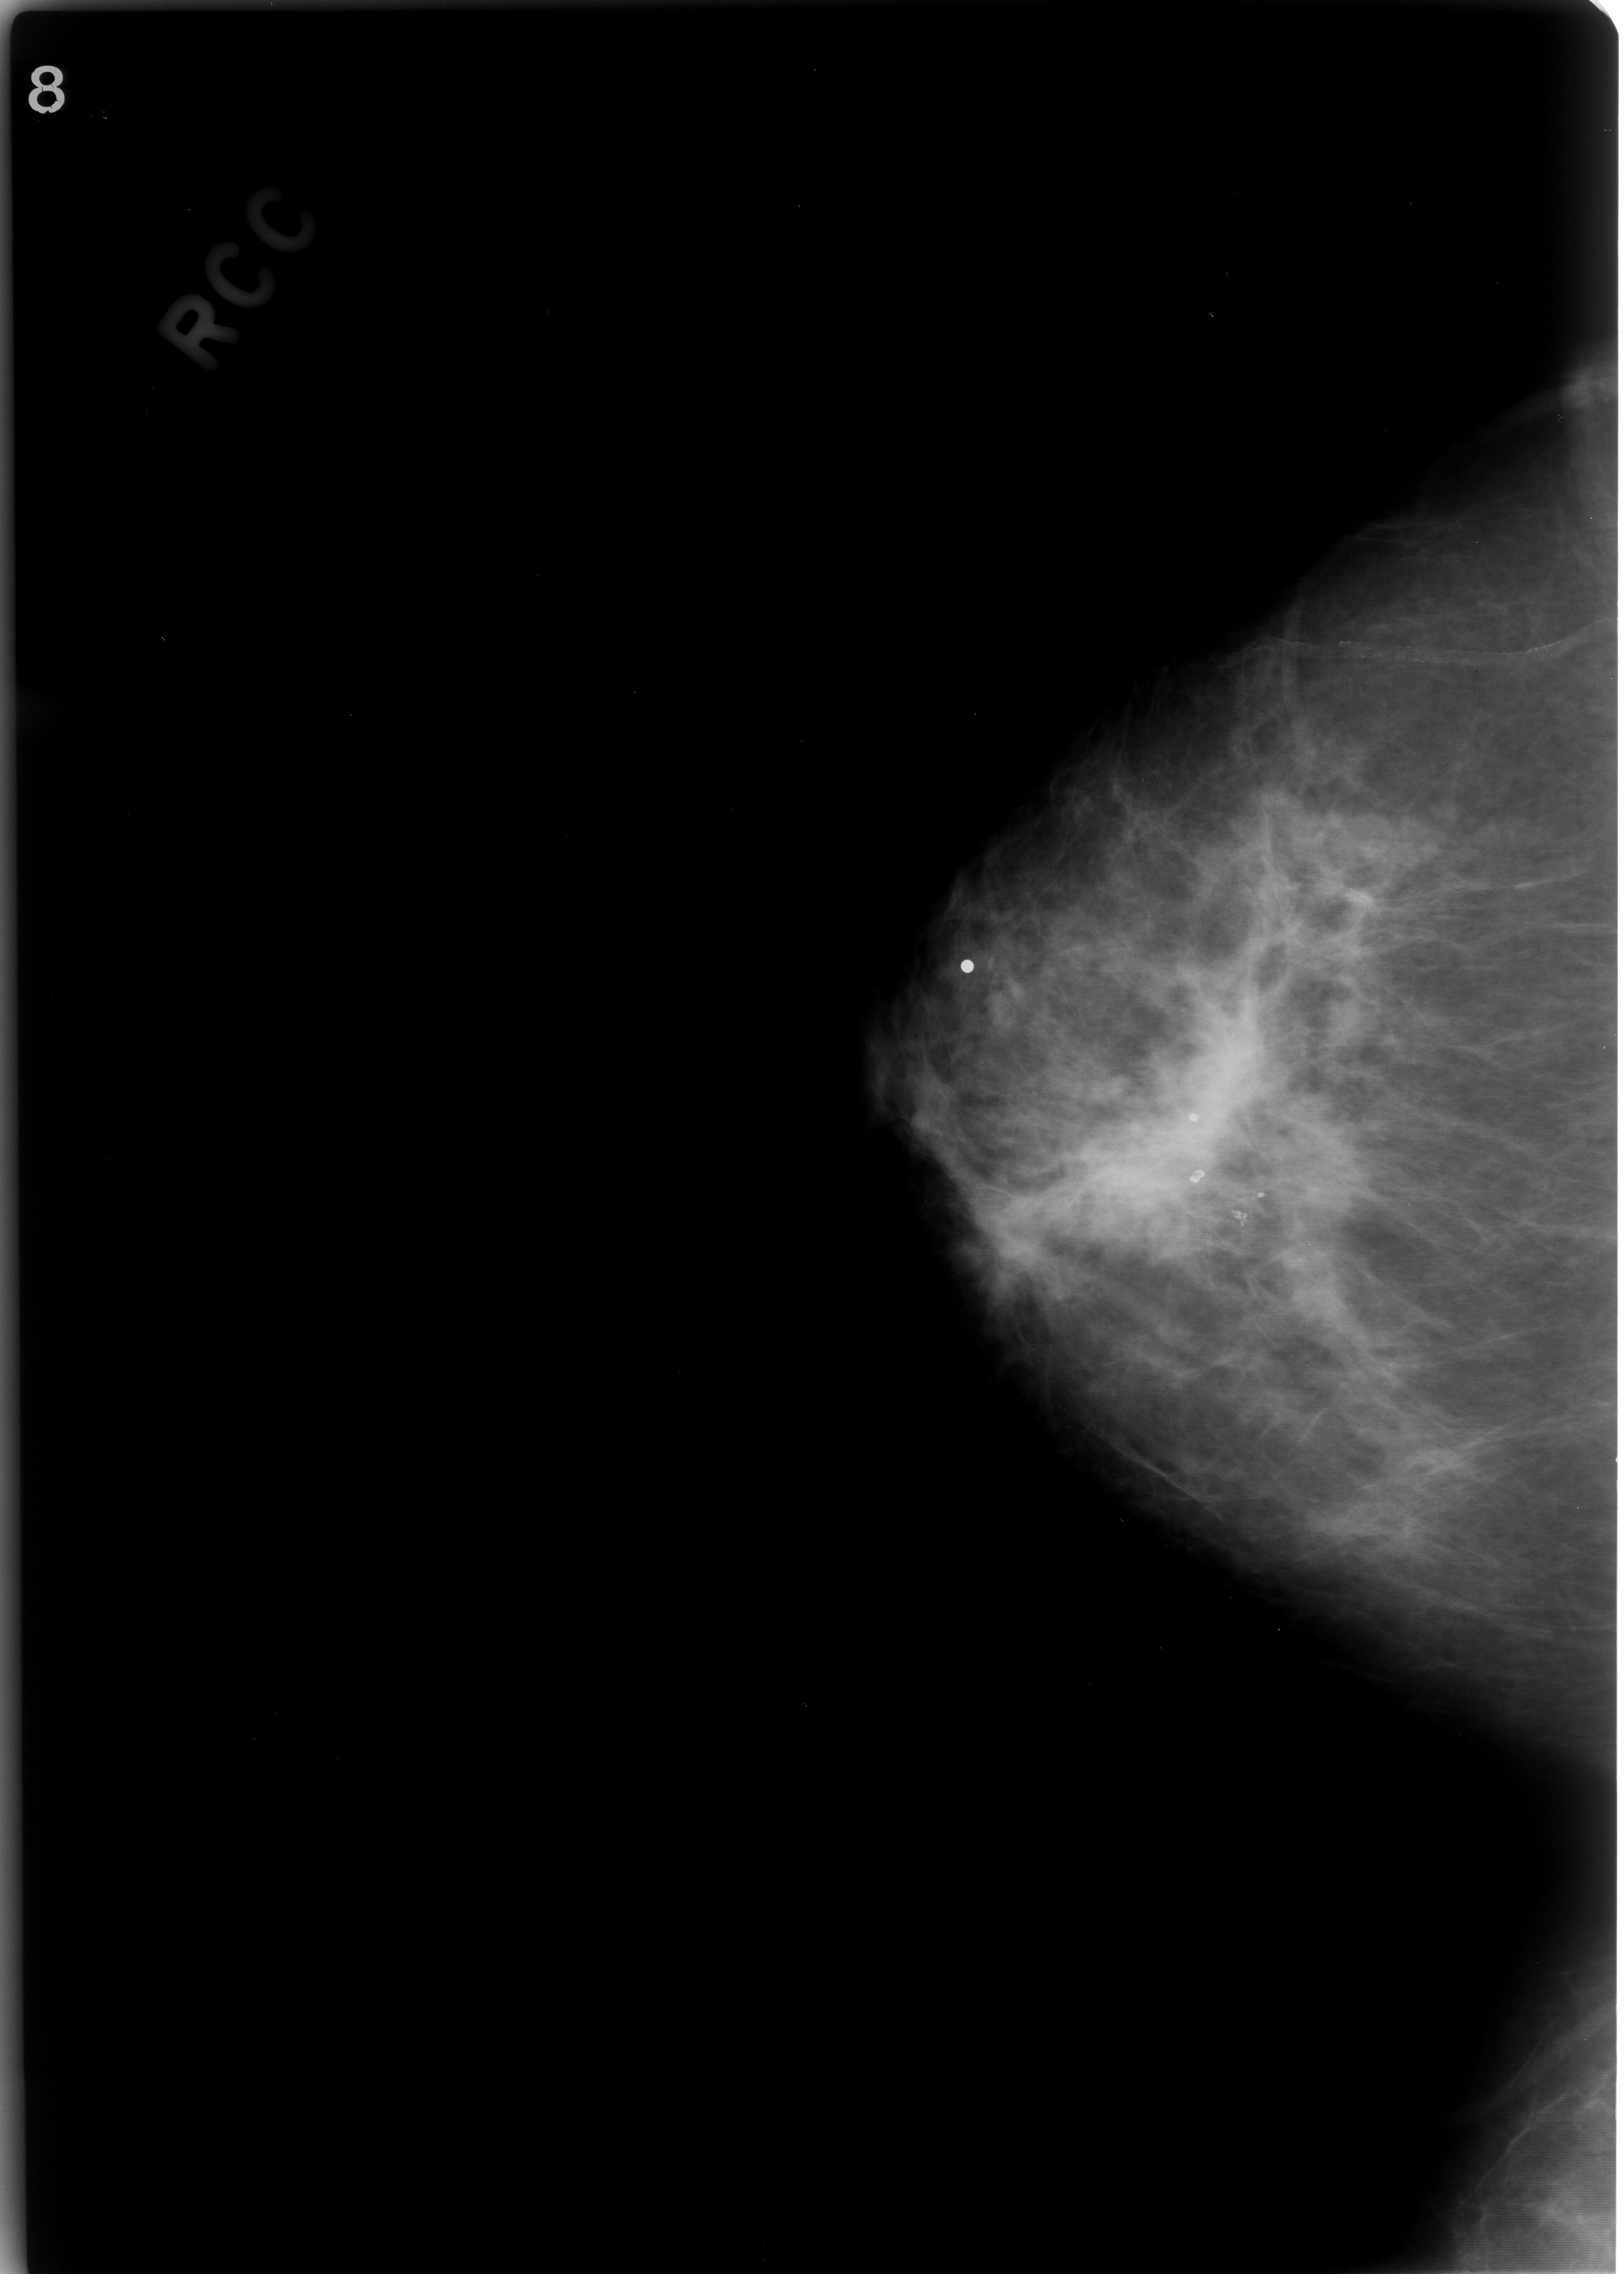
Scanned film-screen mammogram; right breast; craniocaudal (CC) view; breast composition: scattered fibroglandular densities (BI-RADS density category 2 of 4); 1624 × 2274 image matrix.
Expert-marked regions of interest on this film, with their recorded descriptors:
- mass, shape asymmetric breast tissue, margins ill defined; BI-RADS assessment category 5; subtlety rating 5 on a 1 (subtle) to 5 (obvious) scale; pathology (as recorded): malignant: bounding box (x1, y1, x2, y2) in pixels: (979, 895, 1393, 1307)